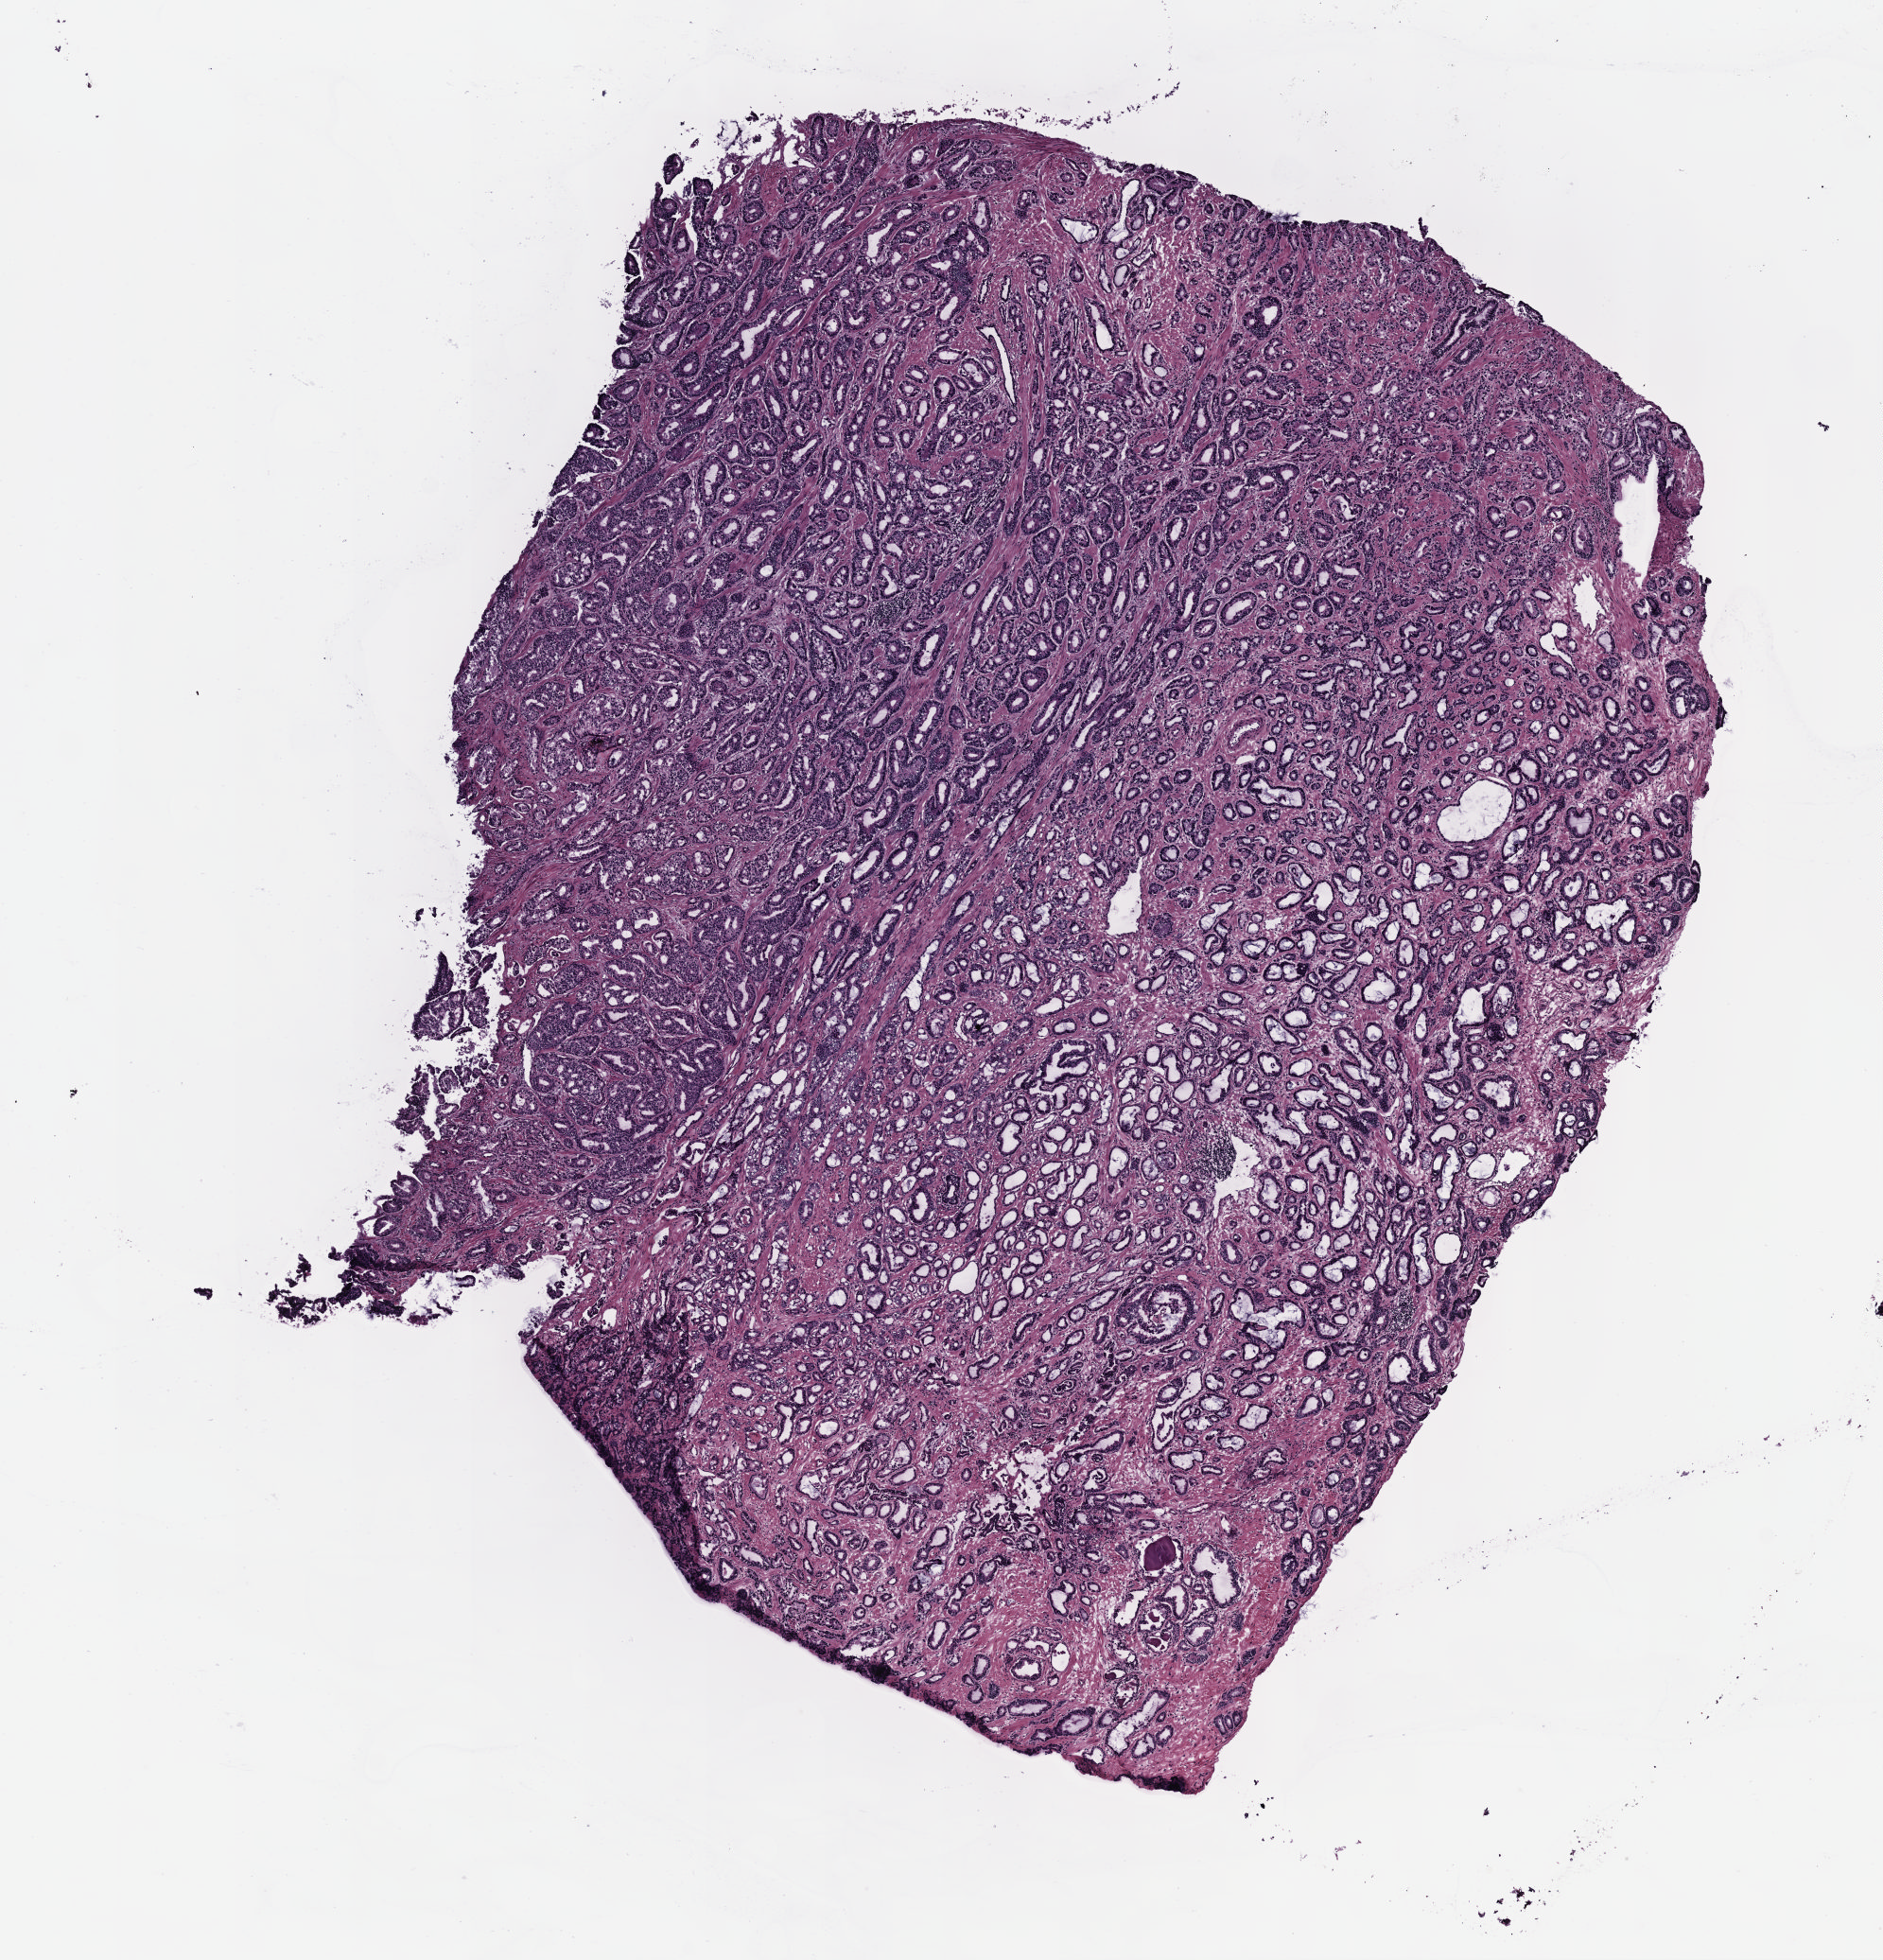
Whole-slide histology image, H&E — whole scanned area (about 8.1 x 8.4 mm, slide scanned at 40x) shown as a low-resolution overview. Frozen section from the top of the tissue portion. Prostate, primary tumour sample. Male patient; age at initial diagnosis 46 years. Gleason score: 8 (3+5). Pathologist review of this section (percent, as recorded): tumour cells 70%, tumour nuclei 80%, normal cells 5%, stromal cells 25%, necrosis 0%. Infiltration values recorded for this section: lymphocyte infiltration 0%, monocyte infiltration 0%, neutrophil infiltration 0%.
* diagnosis: Adenocarcinoma, NOS (prostate gland)